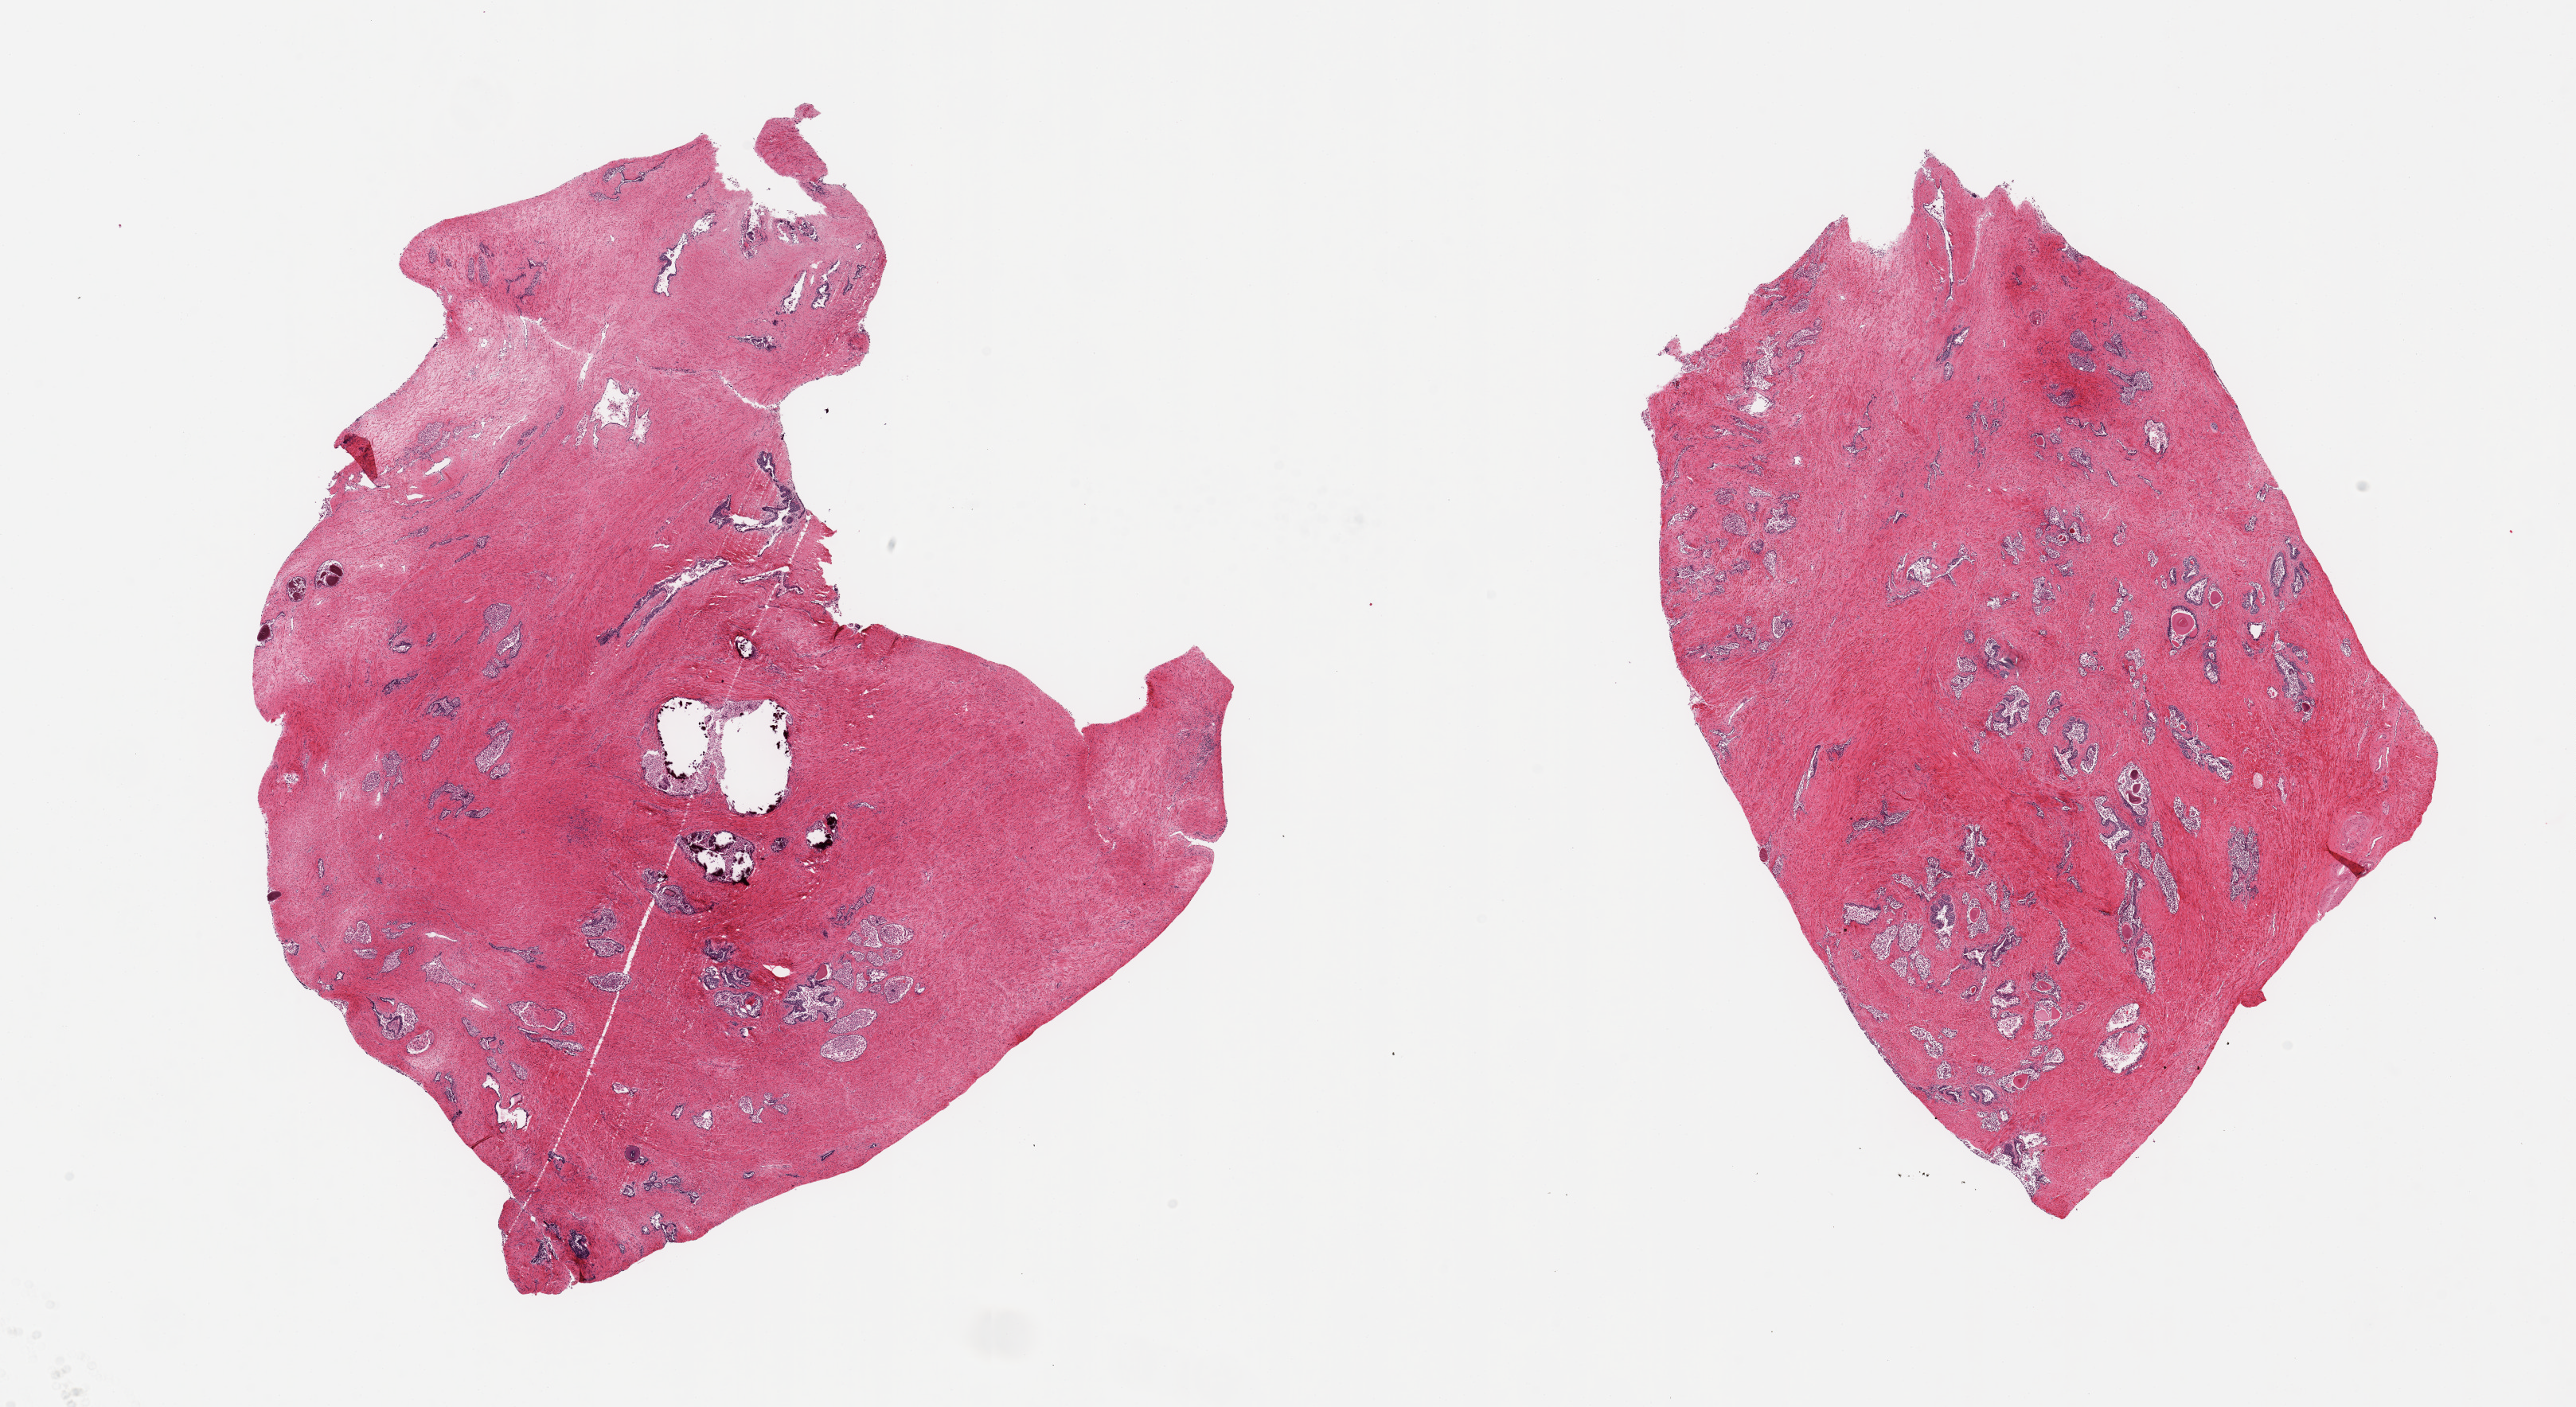
H&E whole-slide image, shown as a low-resolution overview of the whole scanned area (about 25.6 x 14.0 mm); PAXgene-fixed, paraffin-embedded tissue; target tissue: prostate; donor tissue sample.
* review note (as recorded): 2 pieces, glandular component with advanced autolysis